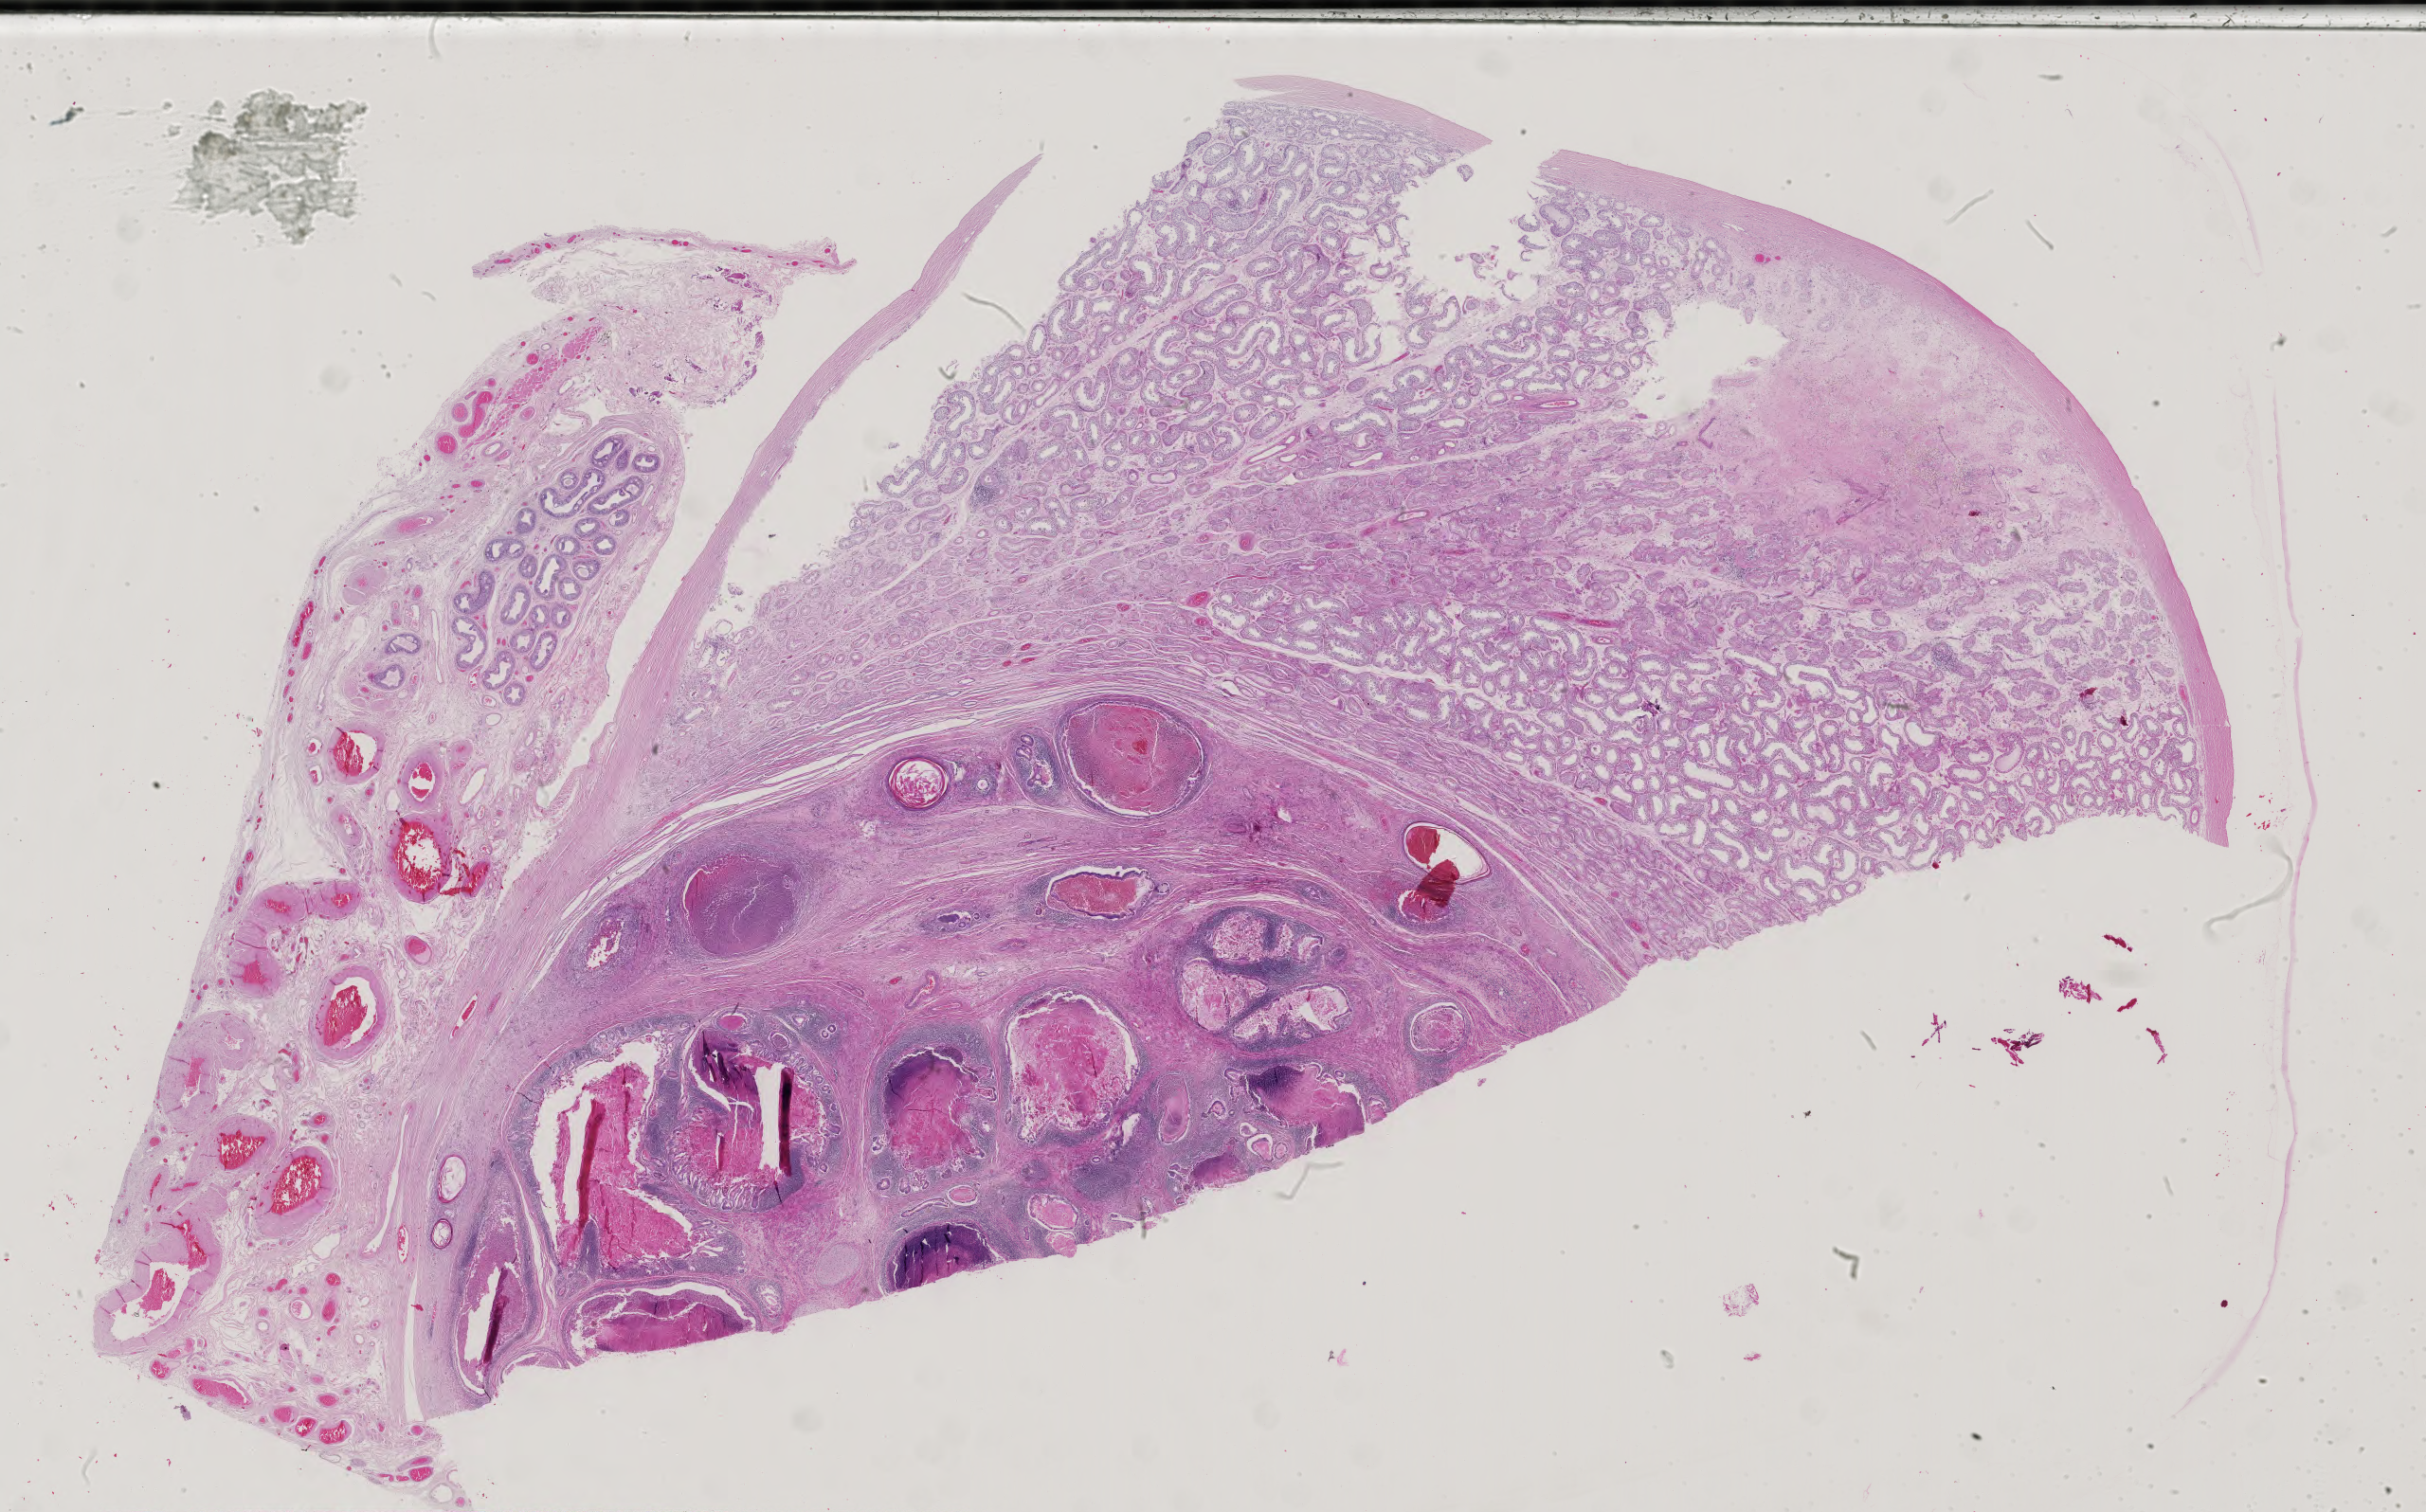
H&E whole-slide image — shown as a low-resolution overview of the whole scanned area (about 37.3 x 23.3 mm, from a 40x scan). Patient sex: male.
Specimen: FFPE section; testis, primary tumour sample.